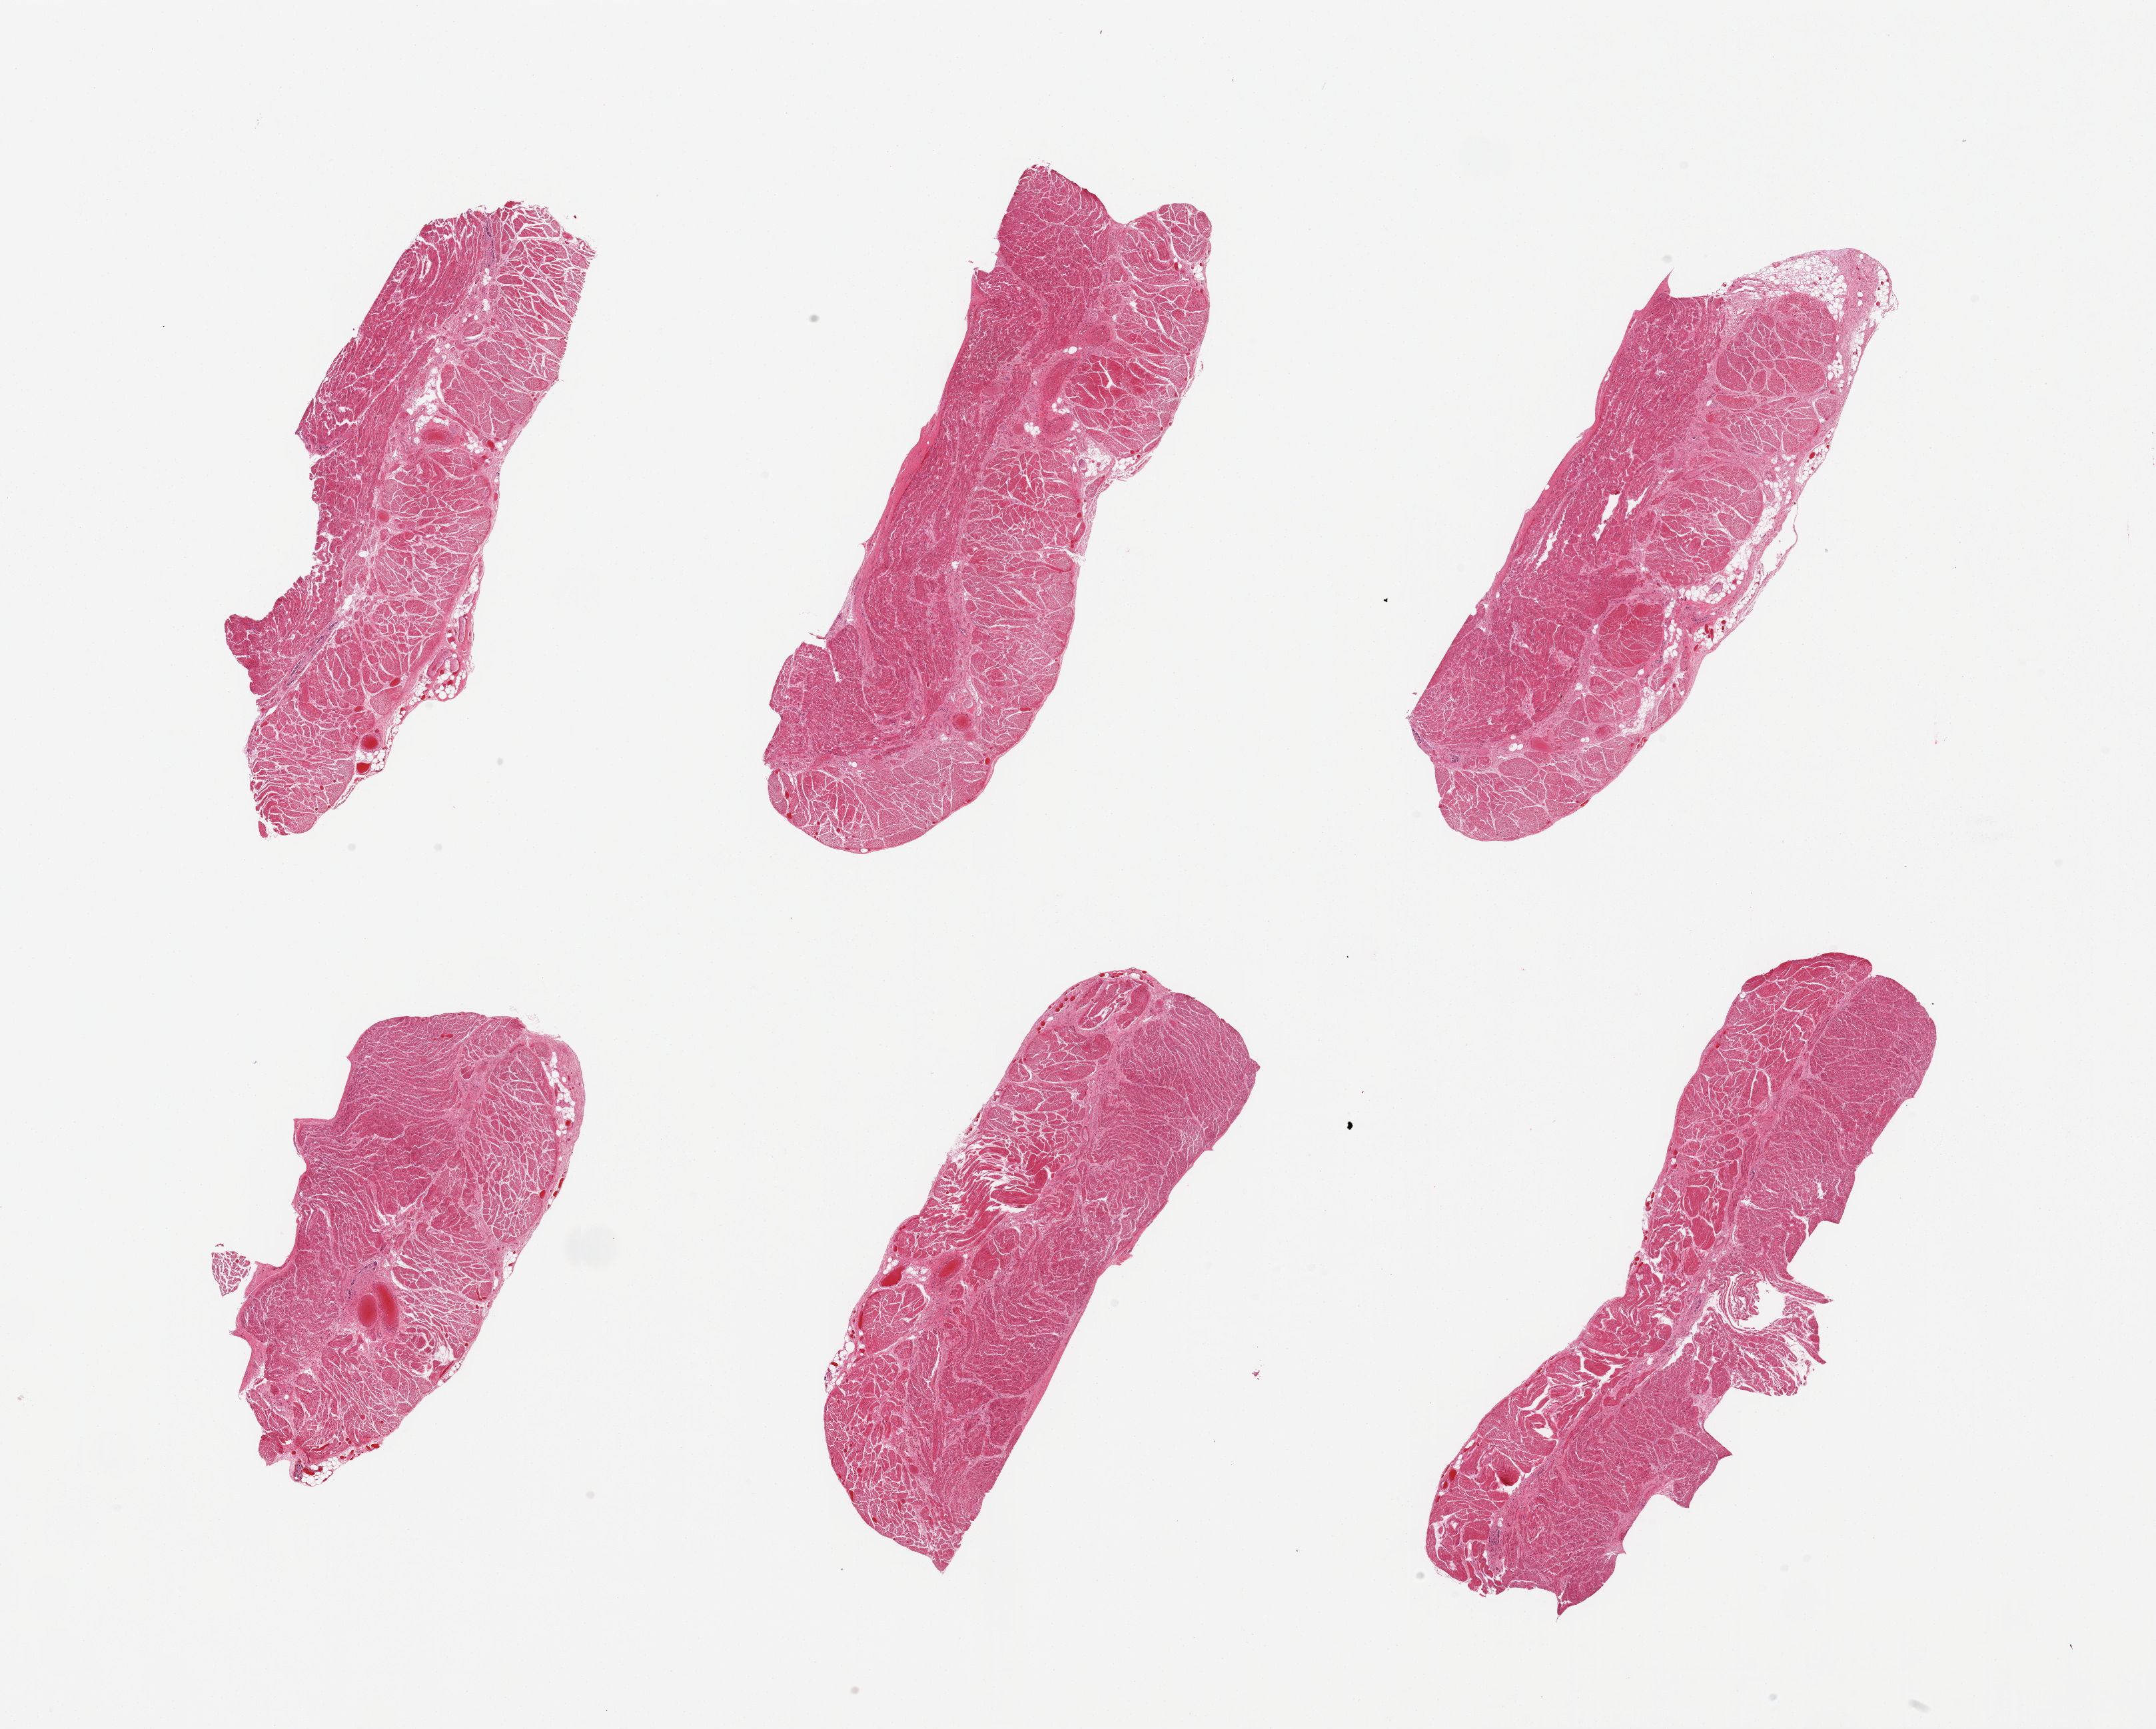
Digitized haematoxylin and eosin-stained section, brightfield — low-resolution overview of the scanned area, about 25.6 x 20.5 mm (from a 20x scan); PAXgene-fixed paraffin-embedded (PFPE) section; sampled site (target tissue): gastroesophageal junction; tissue donor sample. Donor sex: male.
Reviewer comment on this tissue sample: 6 pieces, confirmed target muscularis.